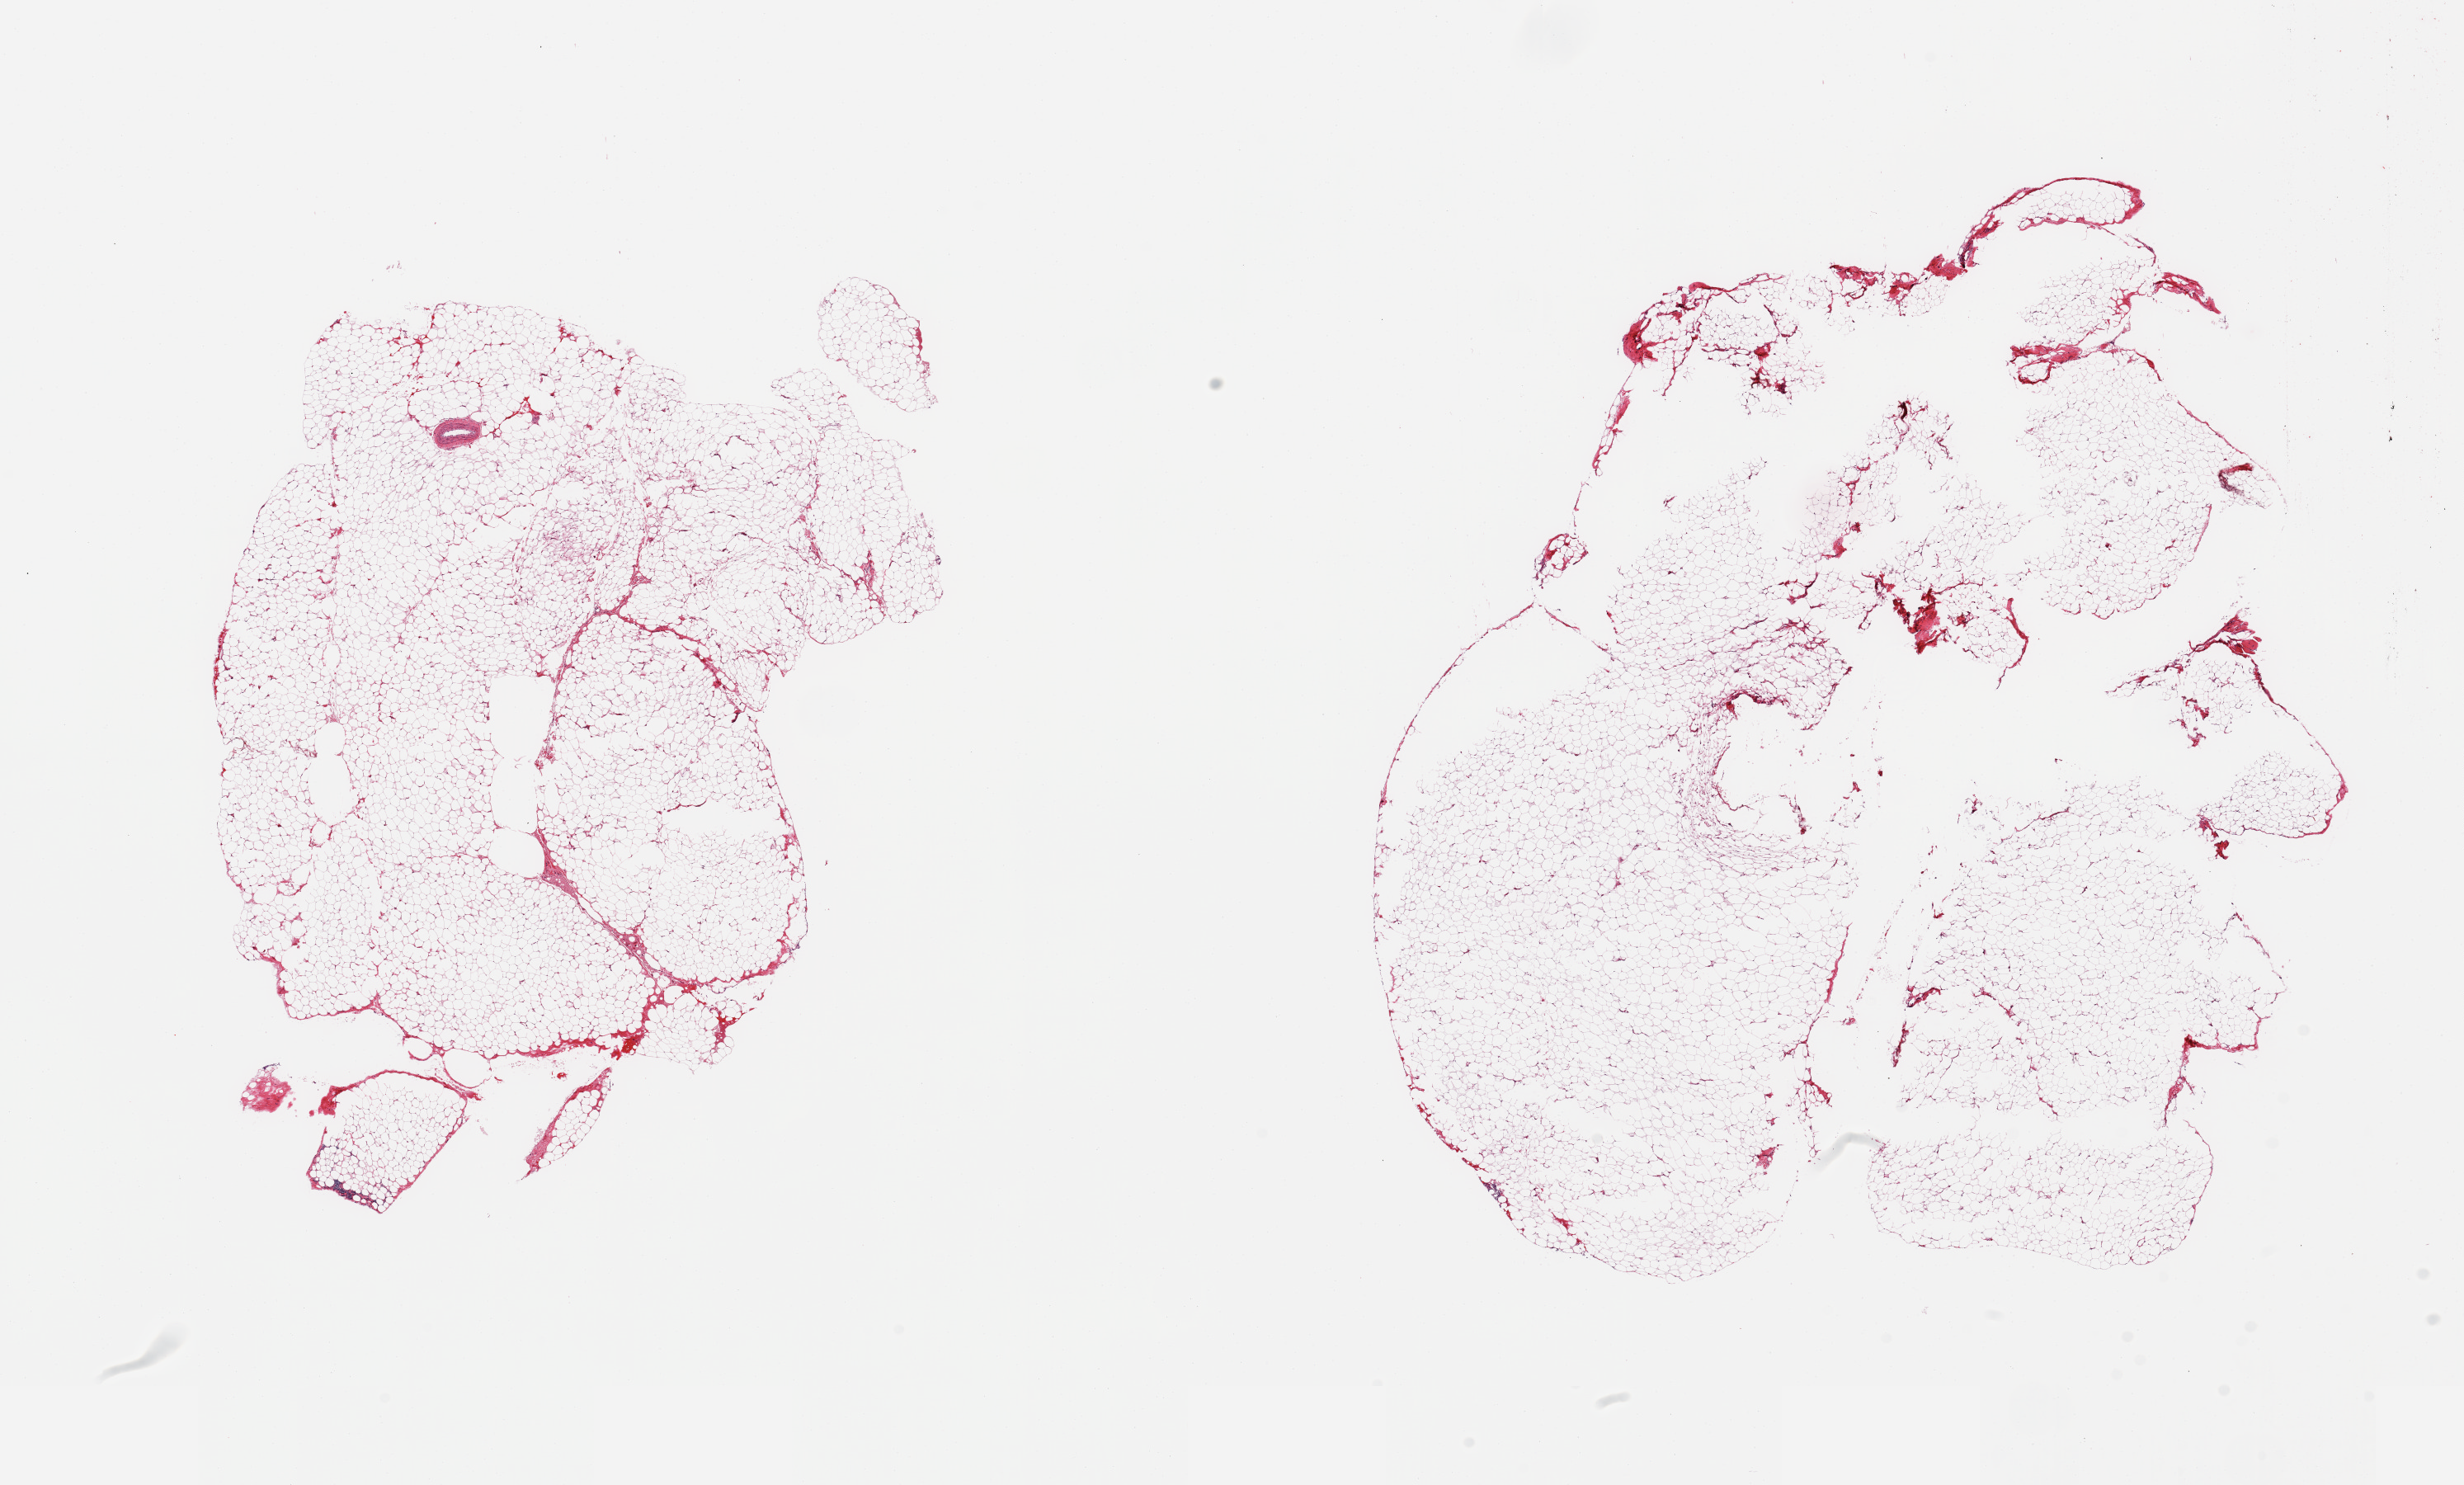
Hematoxylin and eosin (H&E) whole-slide image, brightfield, shown as a low-resolution overview of the whole scanned area (about 23.6 x 14.2 mm); PAXgene-fixed, paraffin-embedded tissue; section of omentum (target tissue); donor tissue sample. Donor sex: male.
Reviewer comment on this tissue sample: 2 pieces; several large tissue holes.